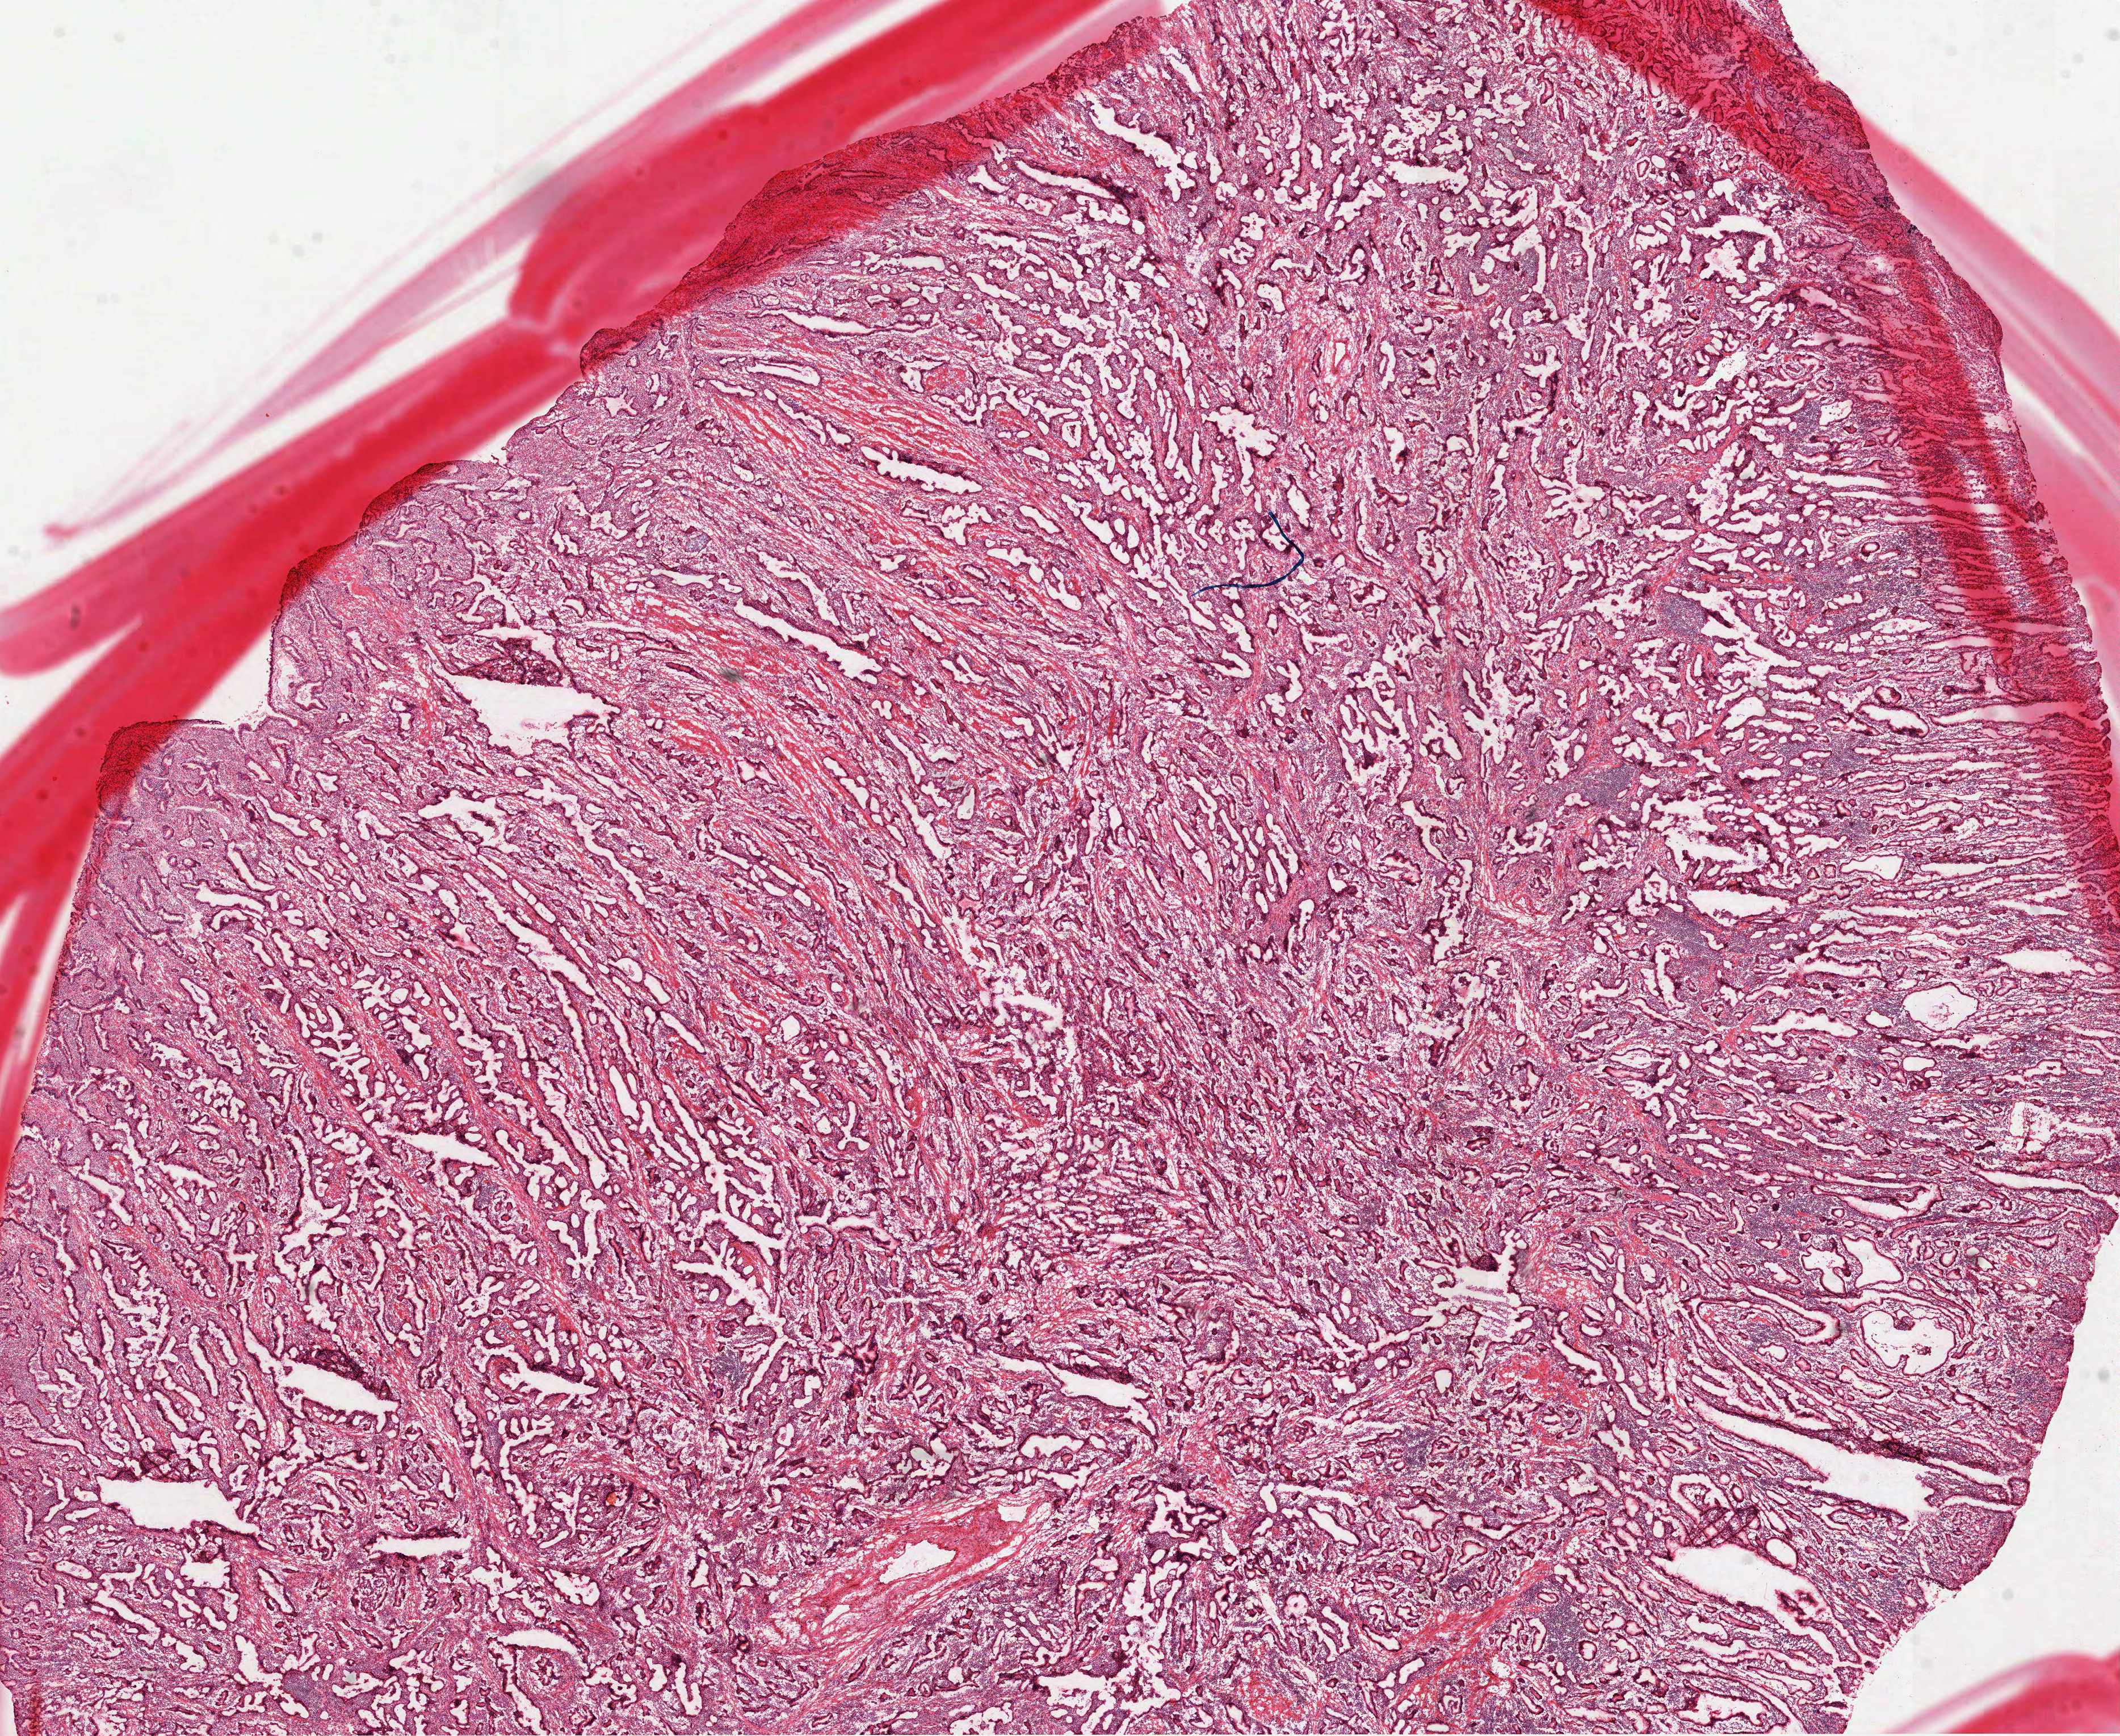
H&E whole-slide image, a low-resolution overview of the entire scanned area, about 15.1 x 12.3 mm (slide scanned at 40x), frozen section, stomach, primary tumour sample. Male patient; age at initial diagnosis 58 years. Histologic grade: G3 (poorly differentiated). Slide review estimates, as recorded: tumour cells 100%, tumour nuclei 65%, normal cells 0%, stromal cells 0%, necrosis 0%. Inflammatory infiltration, as recorded: lymphocyte infiltration 20%, monocyte infiltration 0%, neutrophil infiltration 10%.
Diagnosis: Adenocarcinoma, NOS (cardia, NOS). AJCC pathologic stage: IIA (7th edition). TNM: T3 N0 M0.